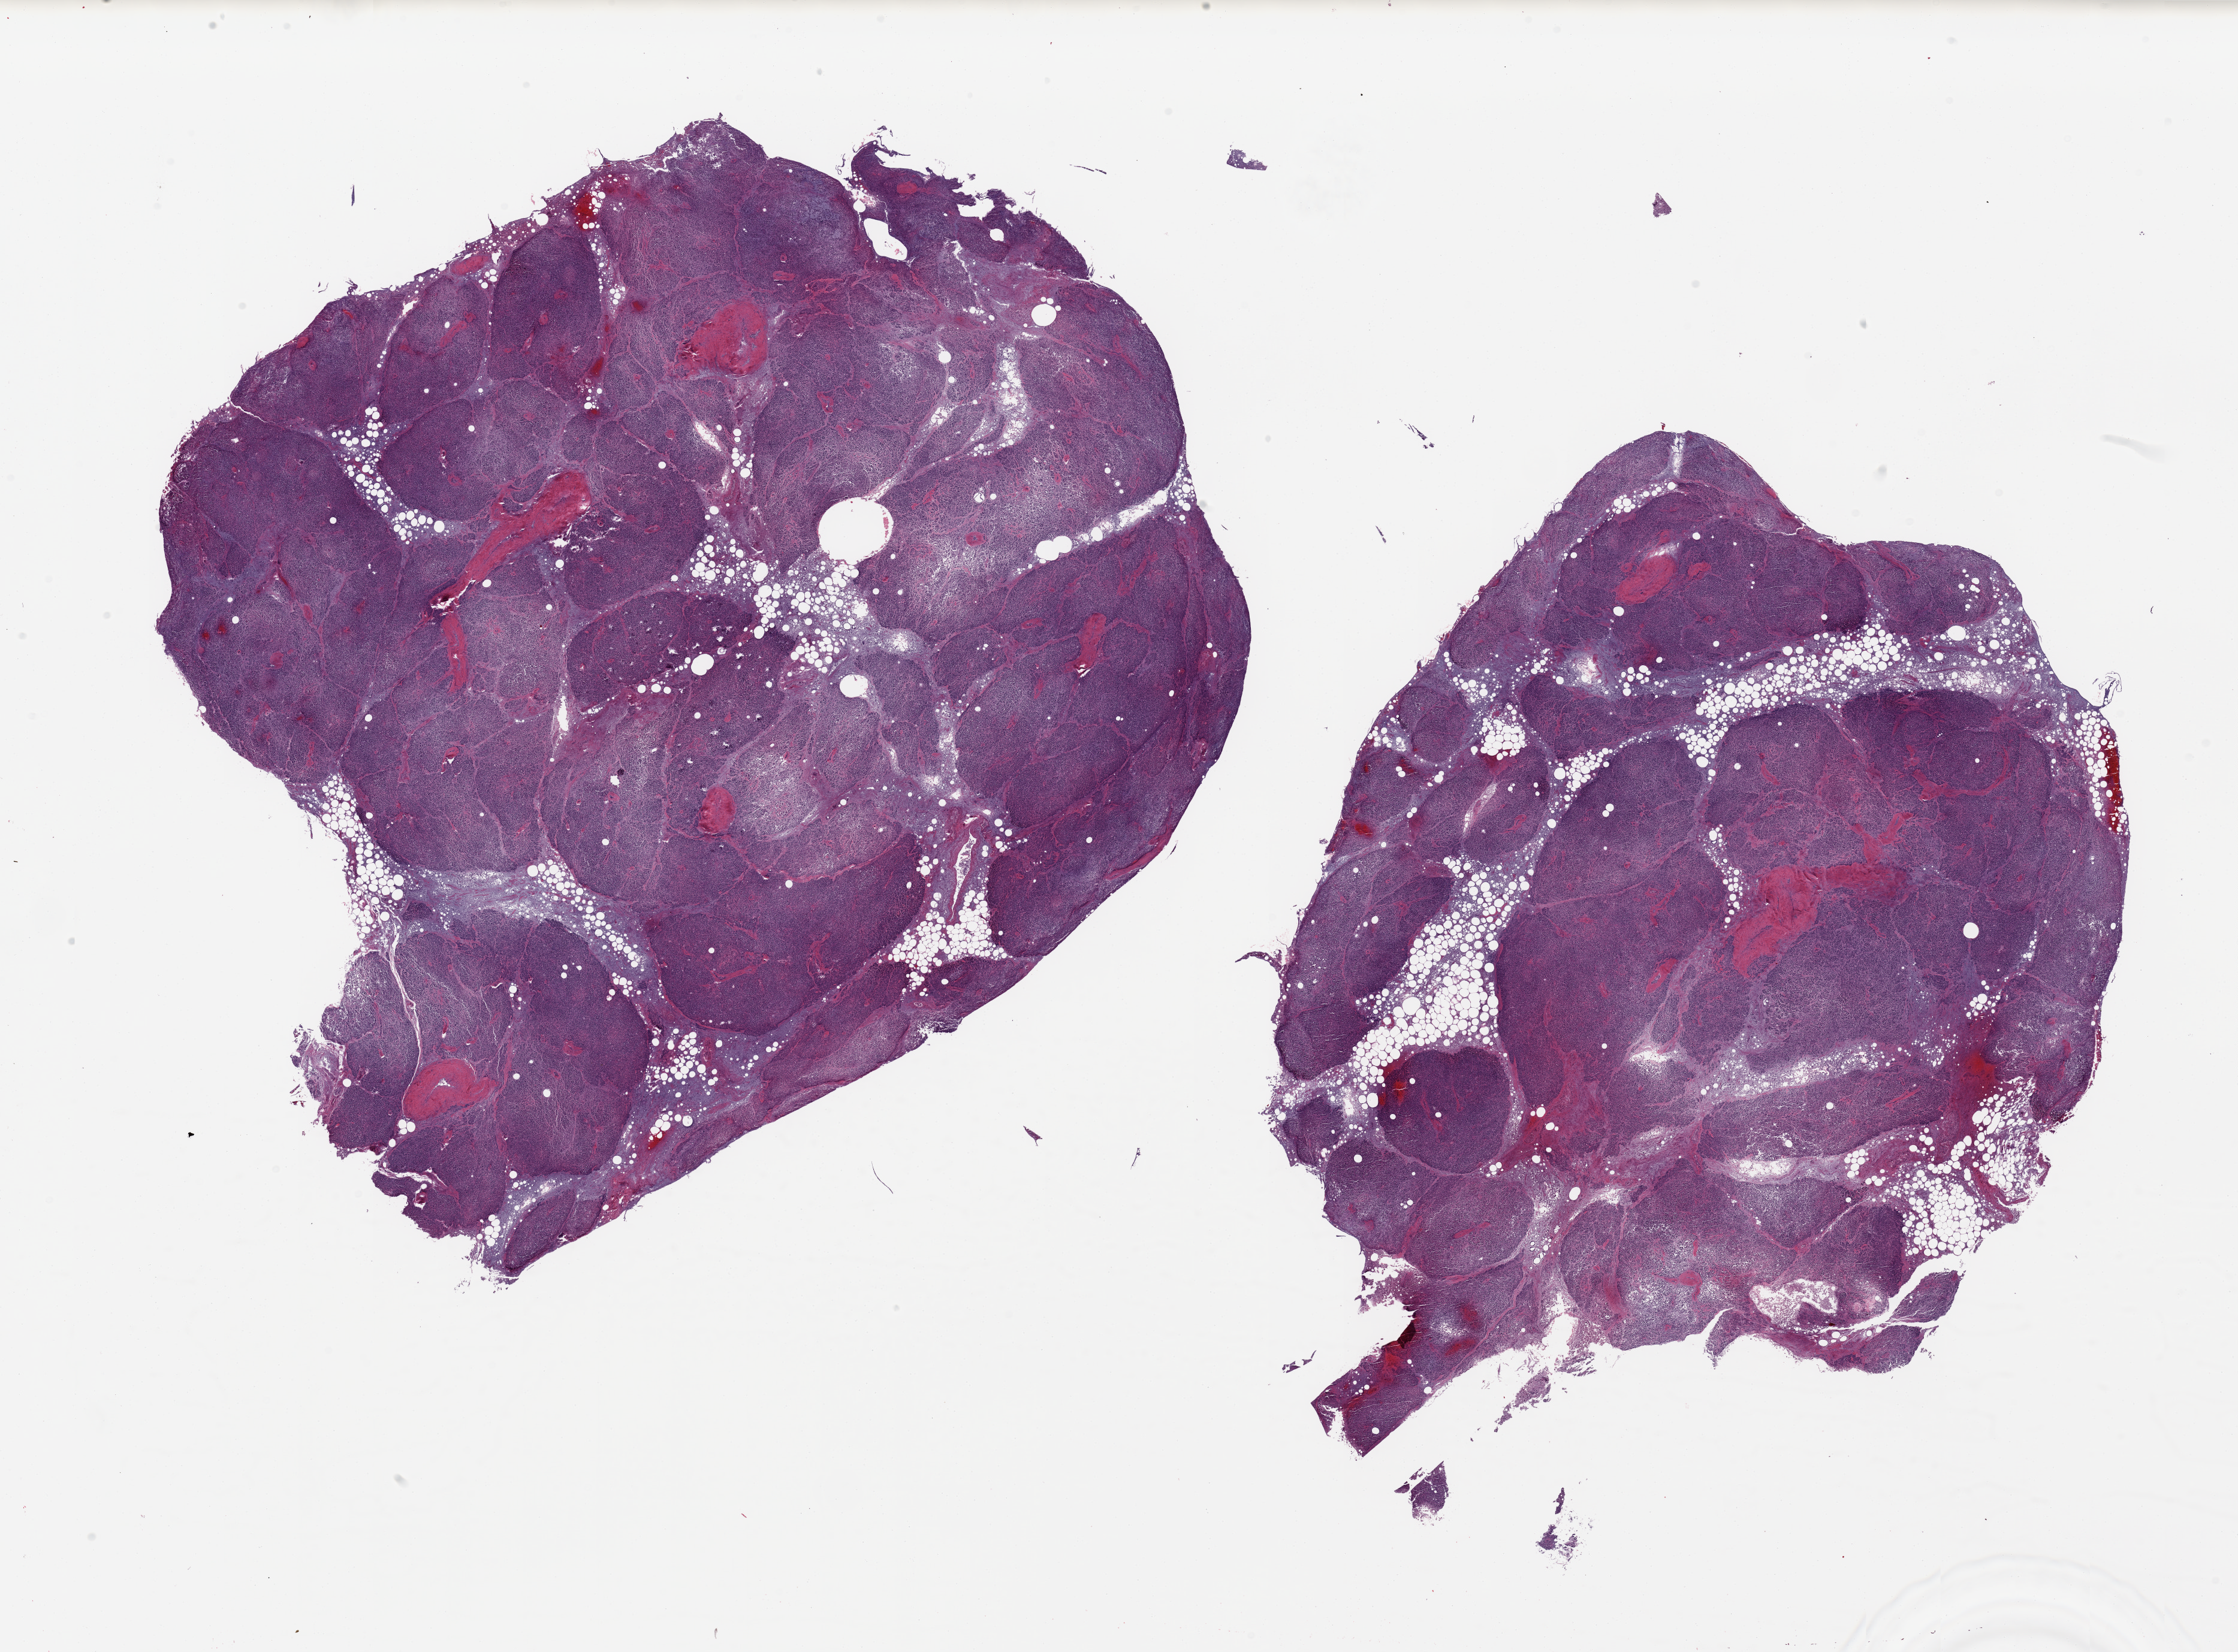
Digitized H&E-stained section, brightfield, a low-resolution overview of the entire scanned area, about 29.5 x 21.8 mm (from a 20x scan). PAXgene-fixed, paraffin-embedded tissue. Section of pancreas (target tissue). Tissue donor sample. Donor: male.
- review note (as recorded): 2 pieces; 10 & 20% internal fat; nuclei preserved better than cytoplasm